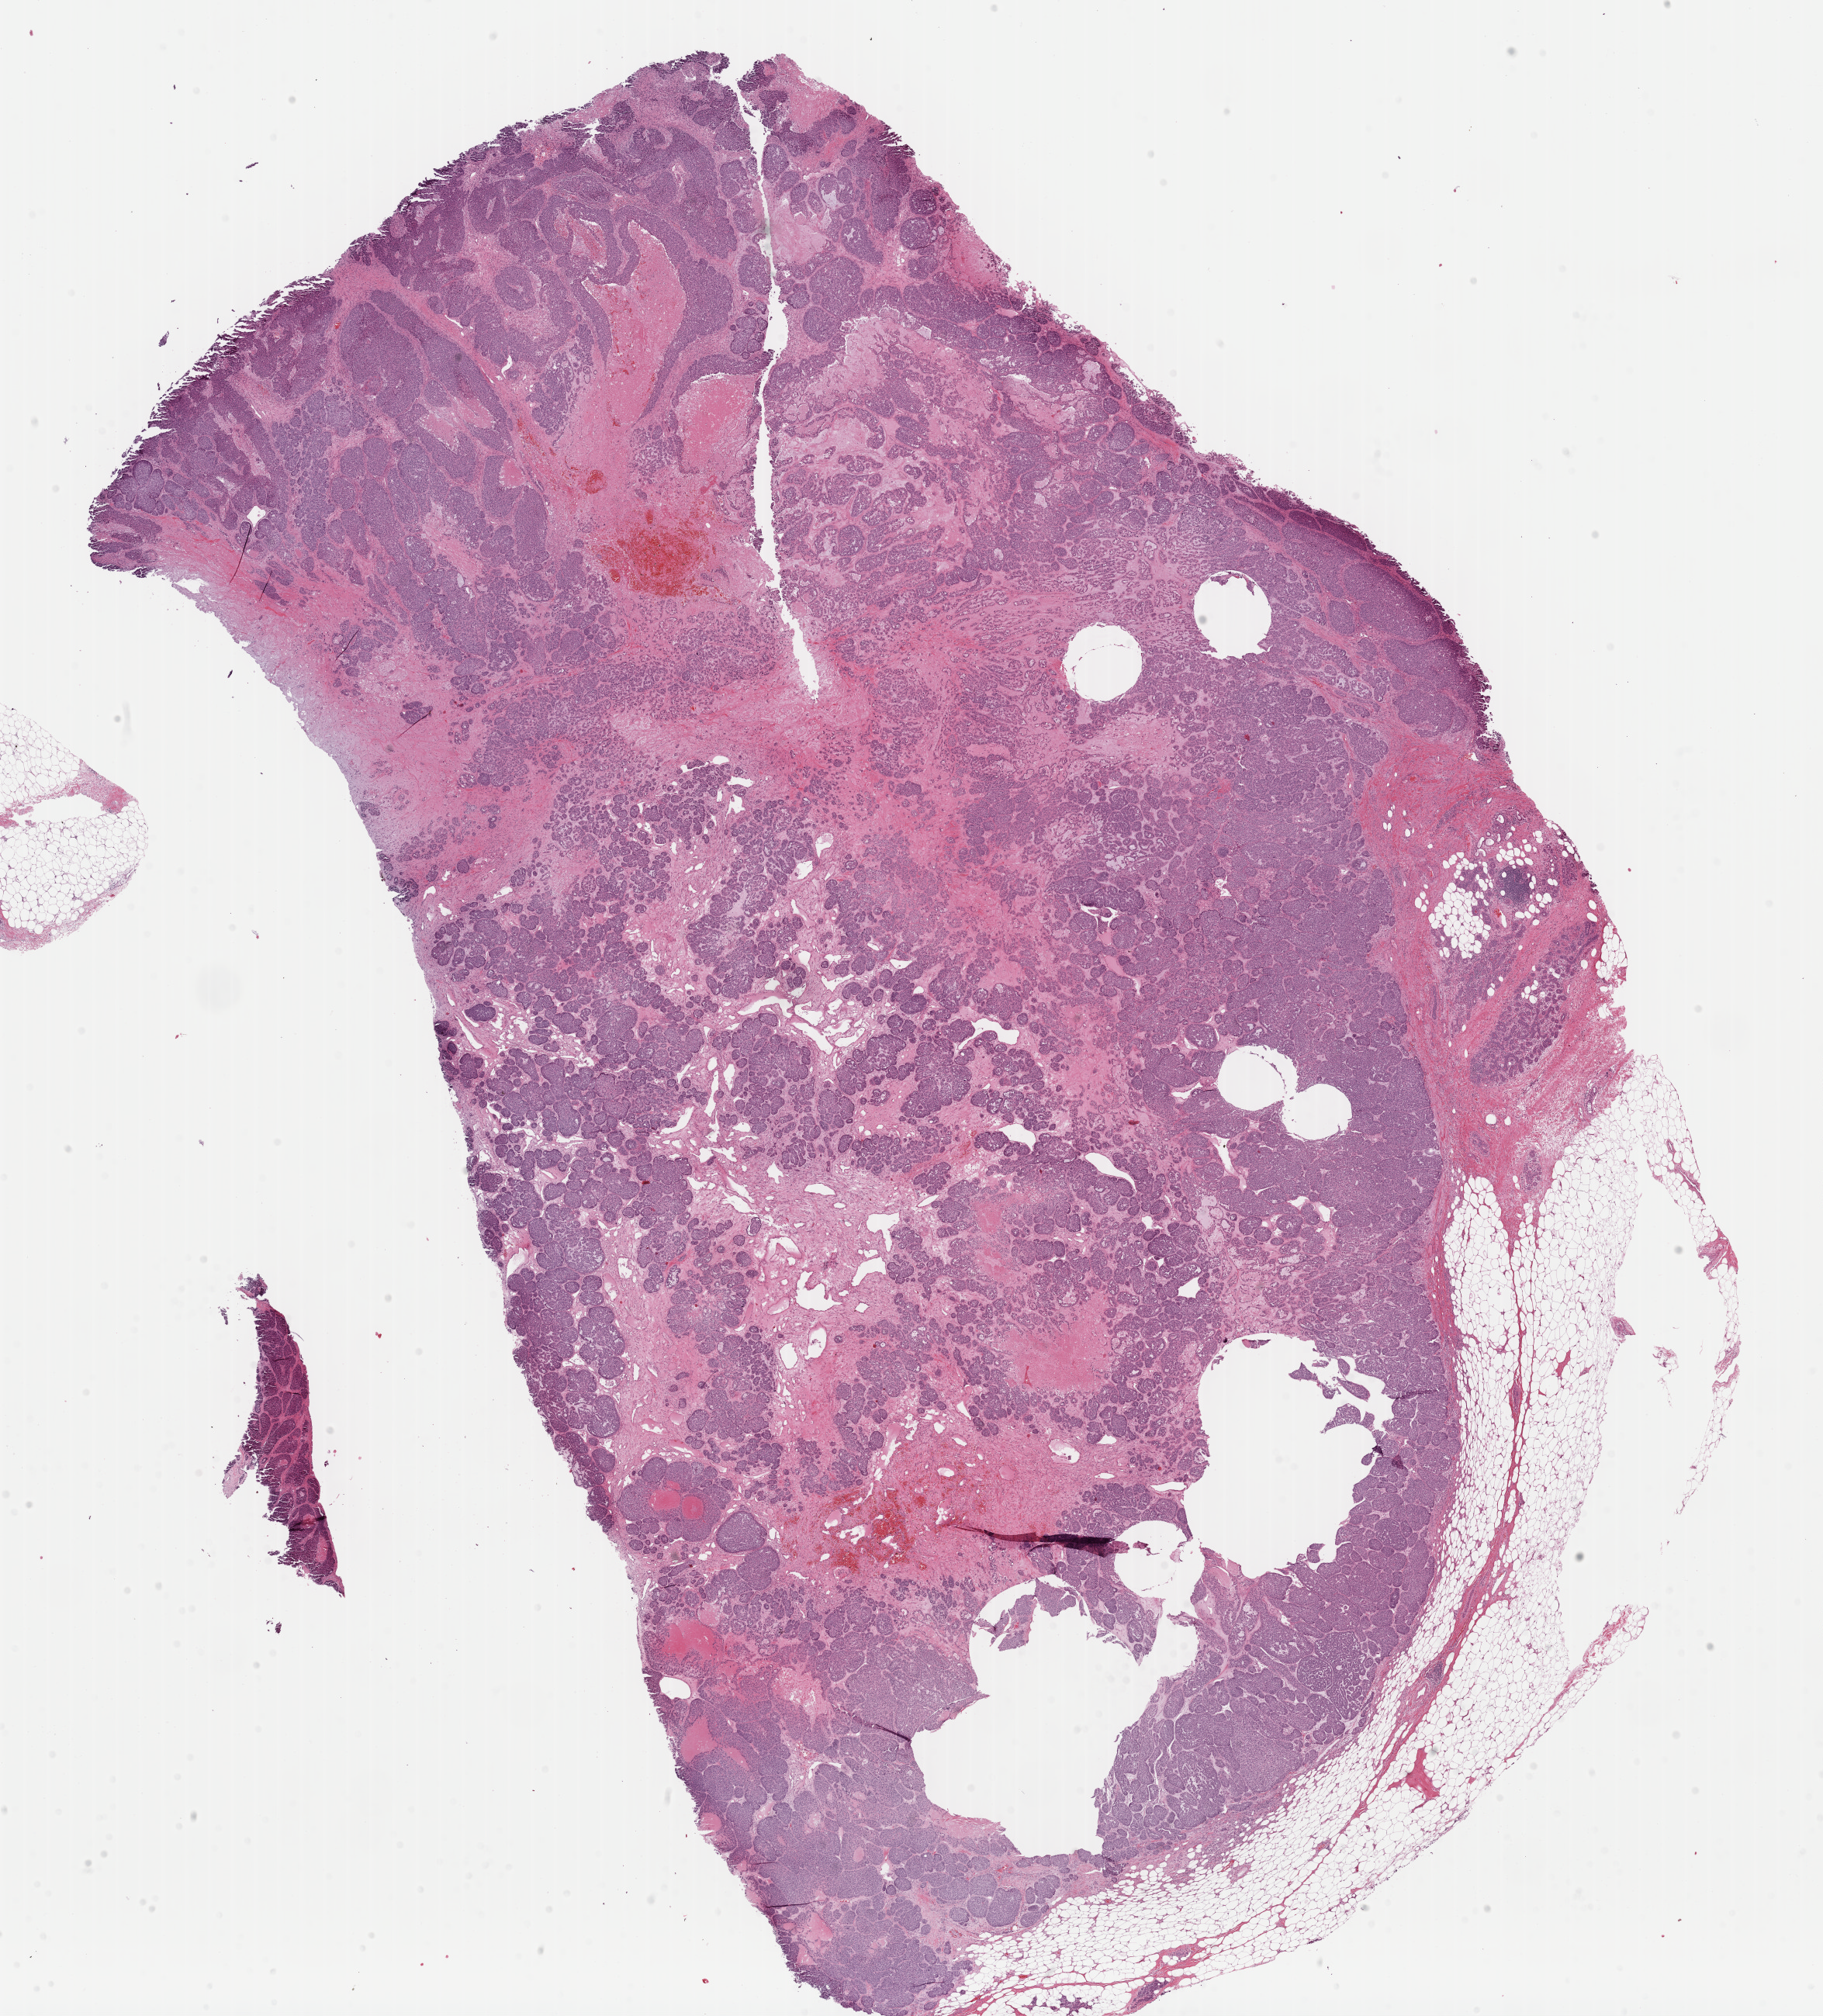
Digitized Hematoxylin and eosin (H&E) stained tissue section (whole slide), shown as a low-resolution overview of the whole scanned area (about 18.6 x 20.5 mm), formalin-fixed paraffin-embedded (FFPE) diagnostic section, sample: primary tumour, breast. Female patient; age at initial diagnosis 43 years.
Histologic diagnosis: Infiltrating duct carcinoma, NOS. AJCC pathologic stage: IIA. Lymph nodes positive (case pathology): 0 of 5 examined.